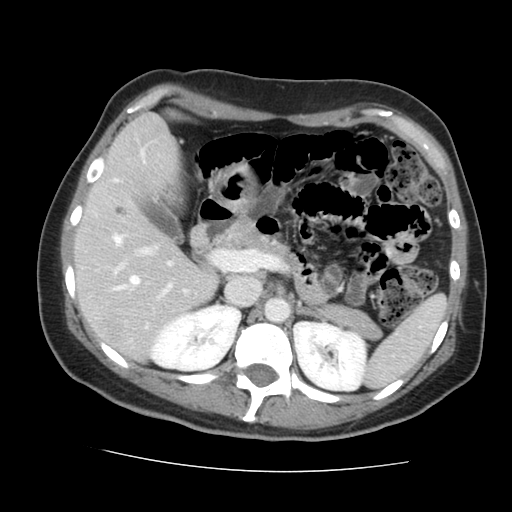
Contrast-enhanced abdominal CT, one axial slice. Position 87 of 144 along the scan axis. Intravenous contrast given. Soft-tissue window (W 400 / L 40 HU). 512 × 512 image matrix. Female patient, age 46 years. Case-level facts recorded for this patient, not image findings: diagnosis: colorectal cancer liver metastases, imaged before liver resection; multiple liver metastases: no; largest metastasis: 2.8 cm; disease in both lobes: no.
Structures marked on this image (outlined manually by an expert reader):
- hepatic veins: bounding box <115,152,143,288> (left, top, right, bottom; pixels)
- liver: <77,116,216,356>
- planned liver remnant (the part of the liver to remain after resection): <77,116,216,356>
- portal vein (with intrahepatic branches): <114,236,226,299>
- liver metastasis: <117,208,123,213>
- liver metastasis: <108,327,116,338>